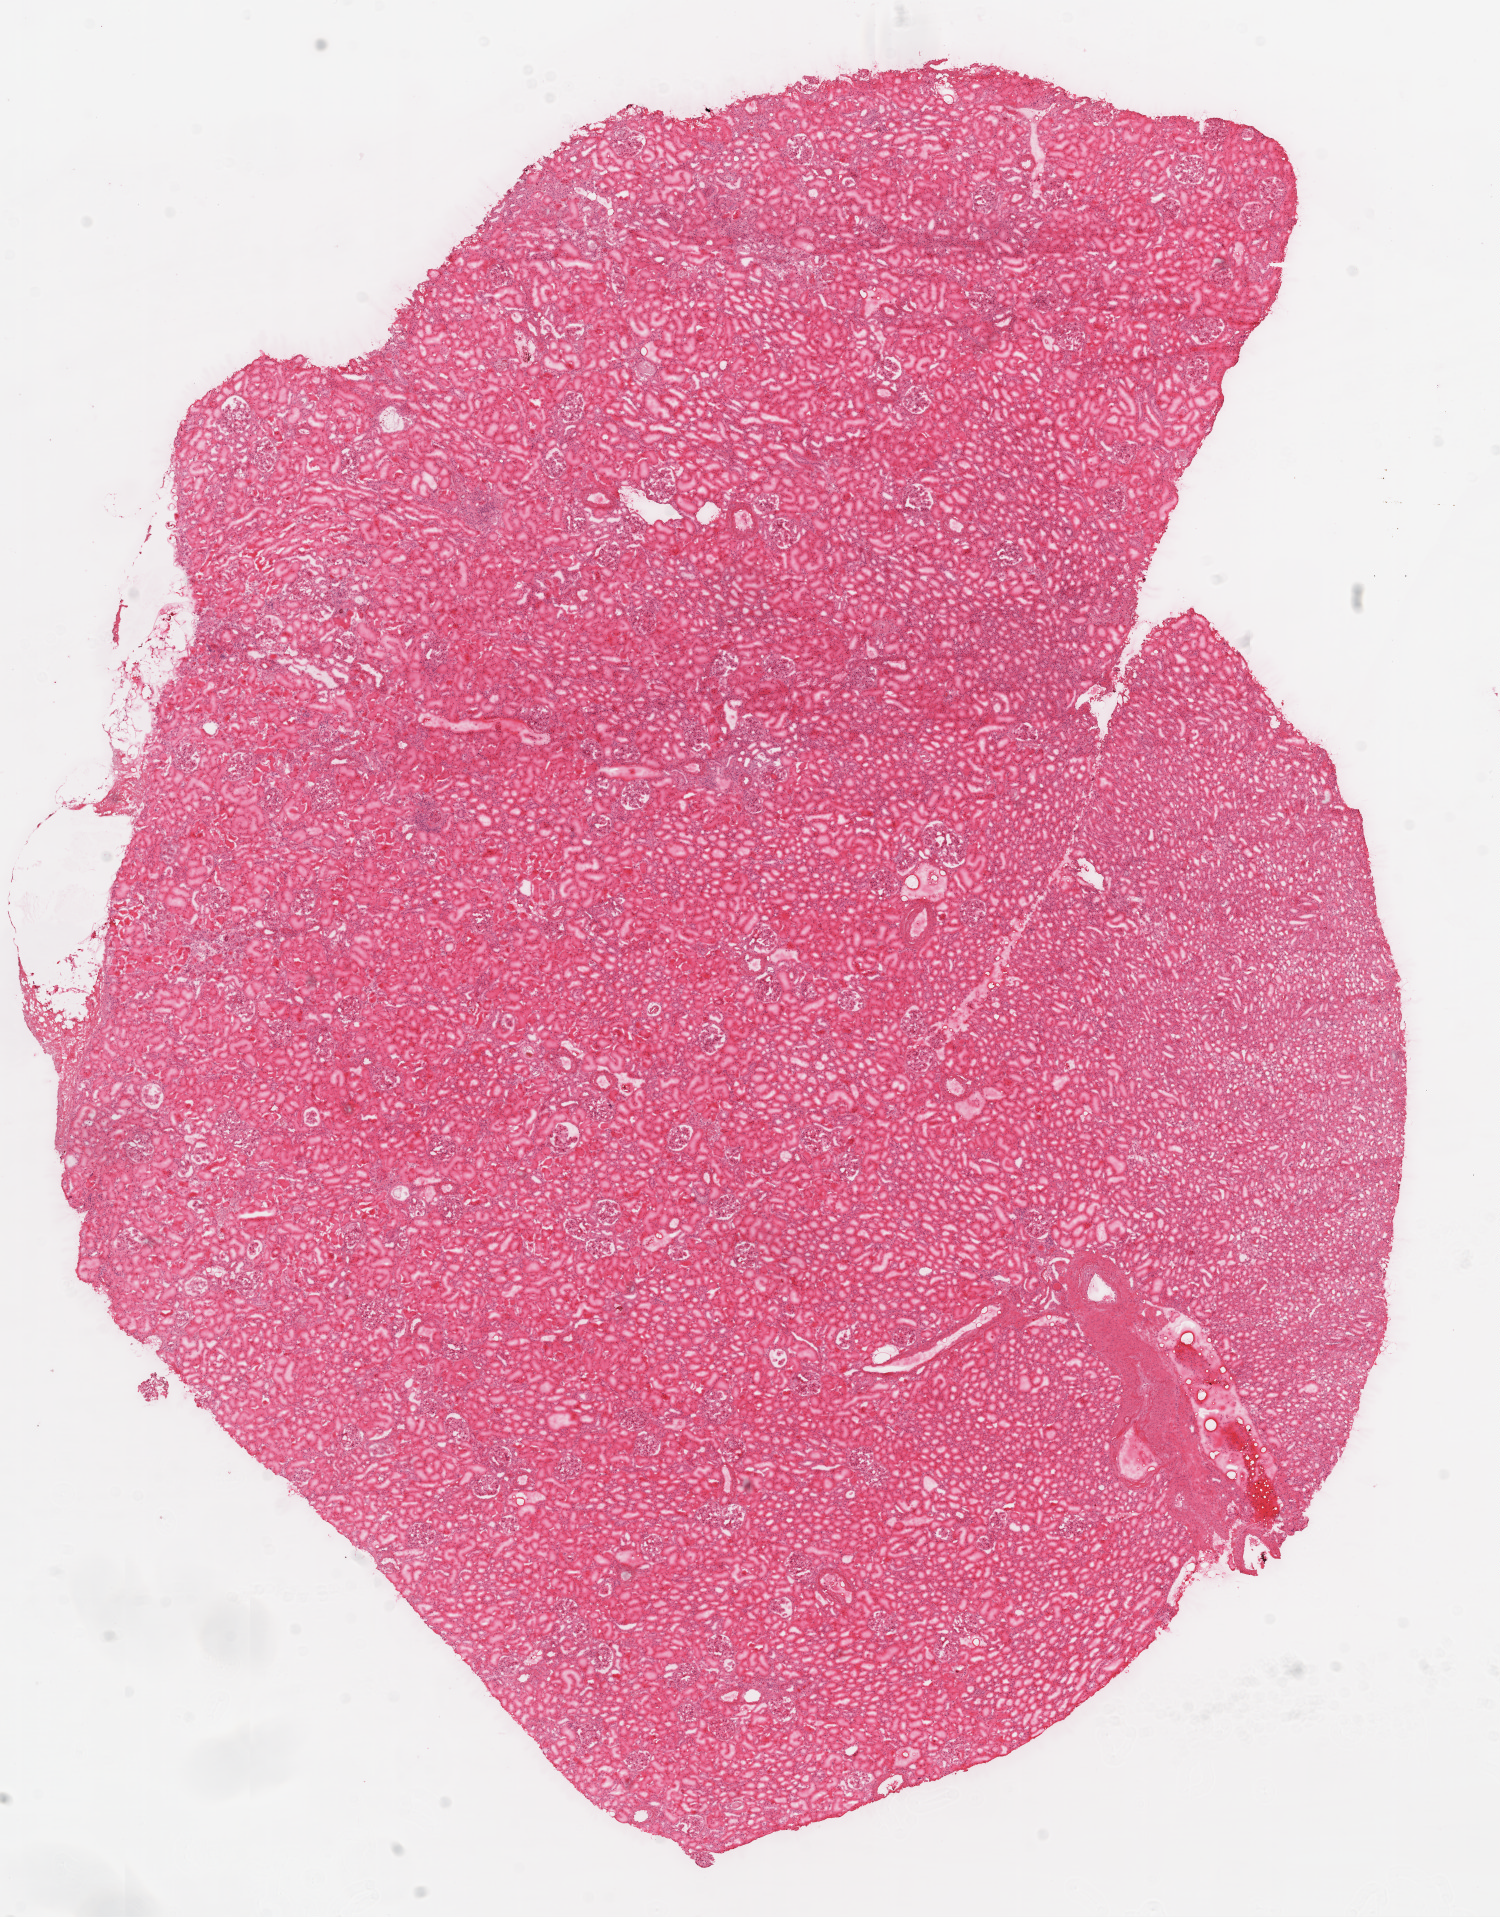
Whole-slide histology image, Hematoxylin and eosin (H&E) stained, shown as a low-resolution overview of the whole scanned area (about 12.0 x 15.4 mm). Frozen section. Kidney, solid tissue normal (non-tumour tissue) sample. Male, age 67 years at initial diagnosis.
- this section: solid tissue normal (non-tumour) sample from the same patient
- patient diagnosis: Clear cell adenocarcinoma, NOS